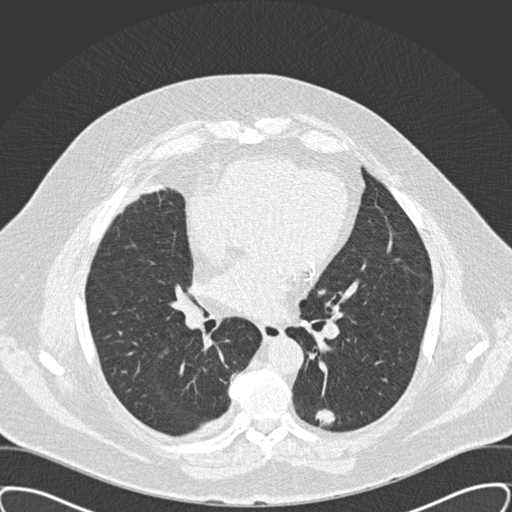
Low-dose screening chest CT, one axial slice. Slice 87 of 159 in the series (ordered by position). Reconstruction kernel B30f. 120 kVp. Lung window (W 1500 / L -600 HU). 2 mm slice thickness. 512 × 512 image matrix, field of view 400 × 400 mm.
Annotated regions visible in this slice (outlined manually by an expert reader):
- lesion 1 (tumor, lower lobe of left lung): box from (x=316, y=409) to (x=335, y=424) px